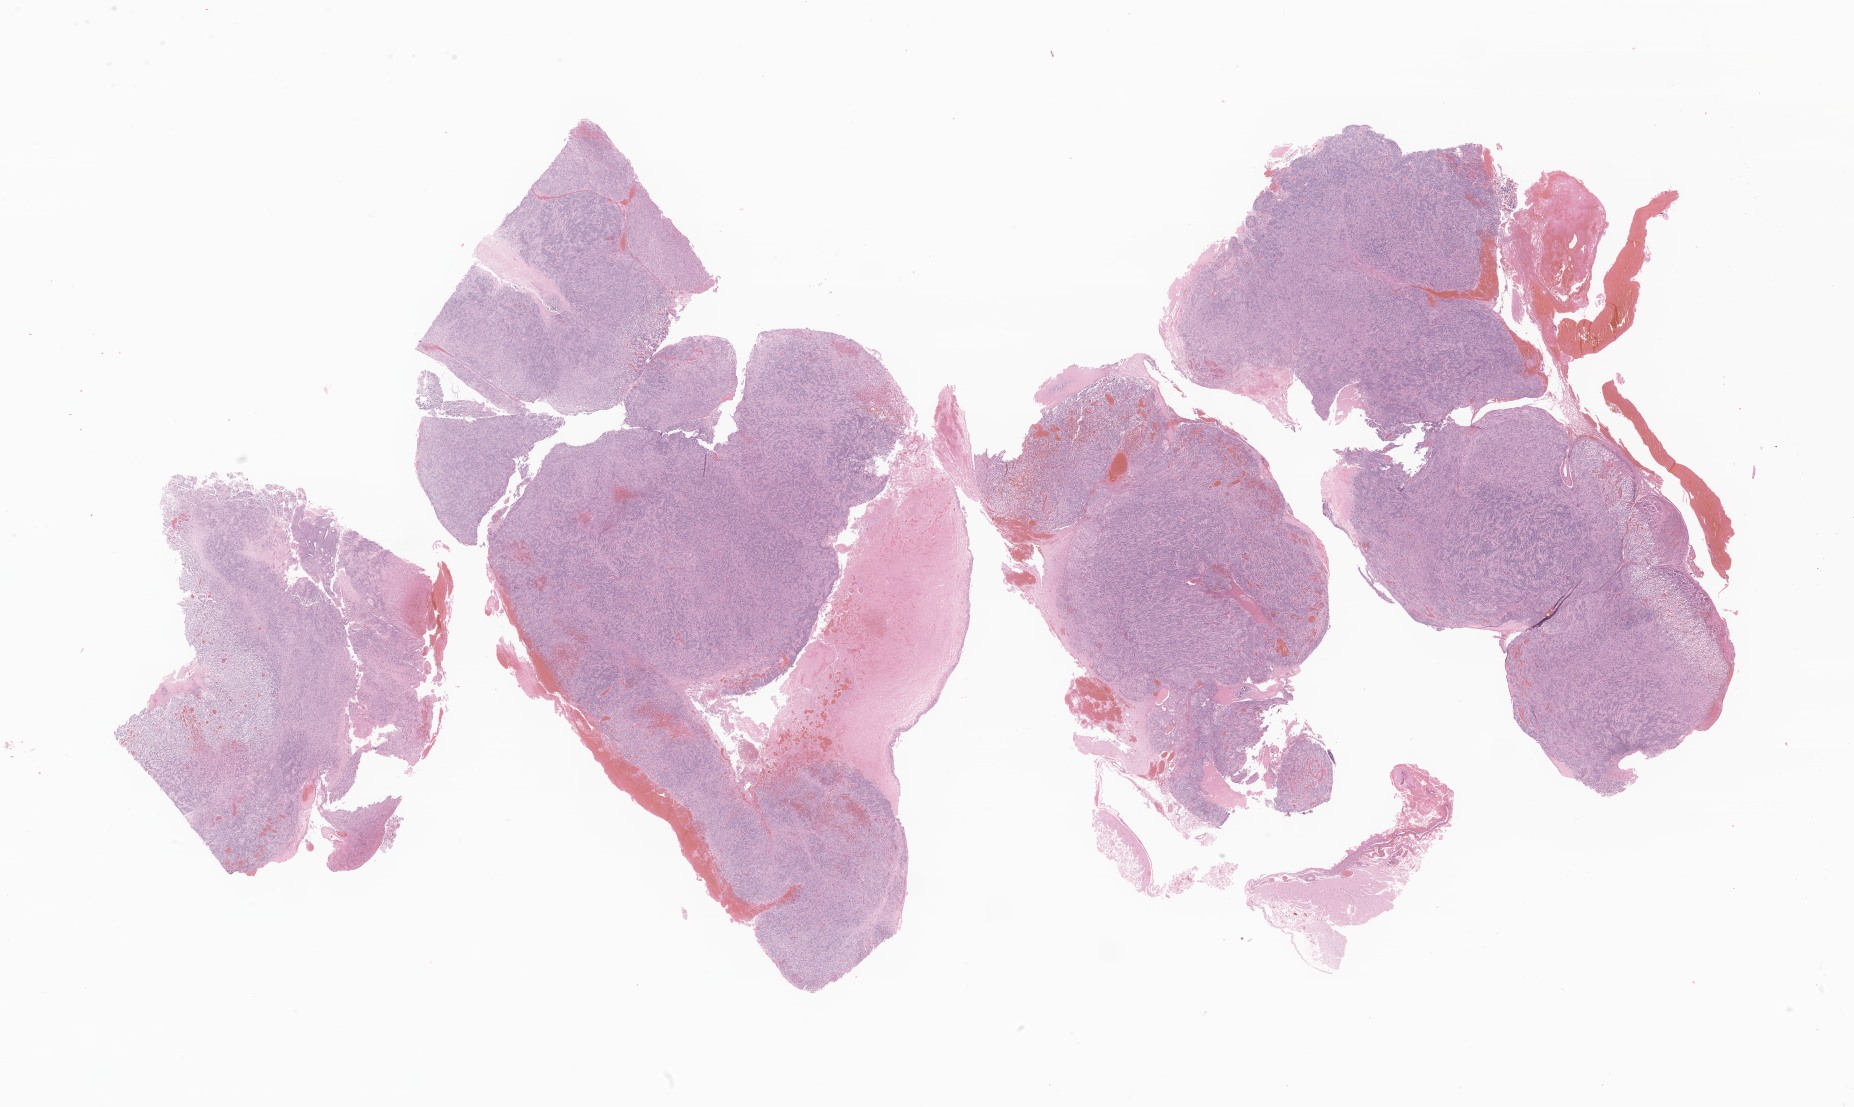
Digitized hematoxylin and eosin (H&E)-stained section of tumor tissue from the frontal lobe — whole scanned area (about 31.3 x 18.7 mm) shown as a low-resolution overview. Formalin-fixed, paraffin-embedded (FFPE) tissue. Female patient, age 762 days.
Diagnosis: Ependymoma, NOS.